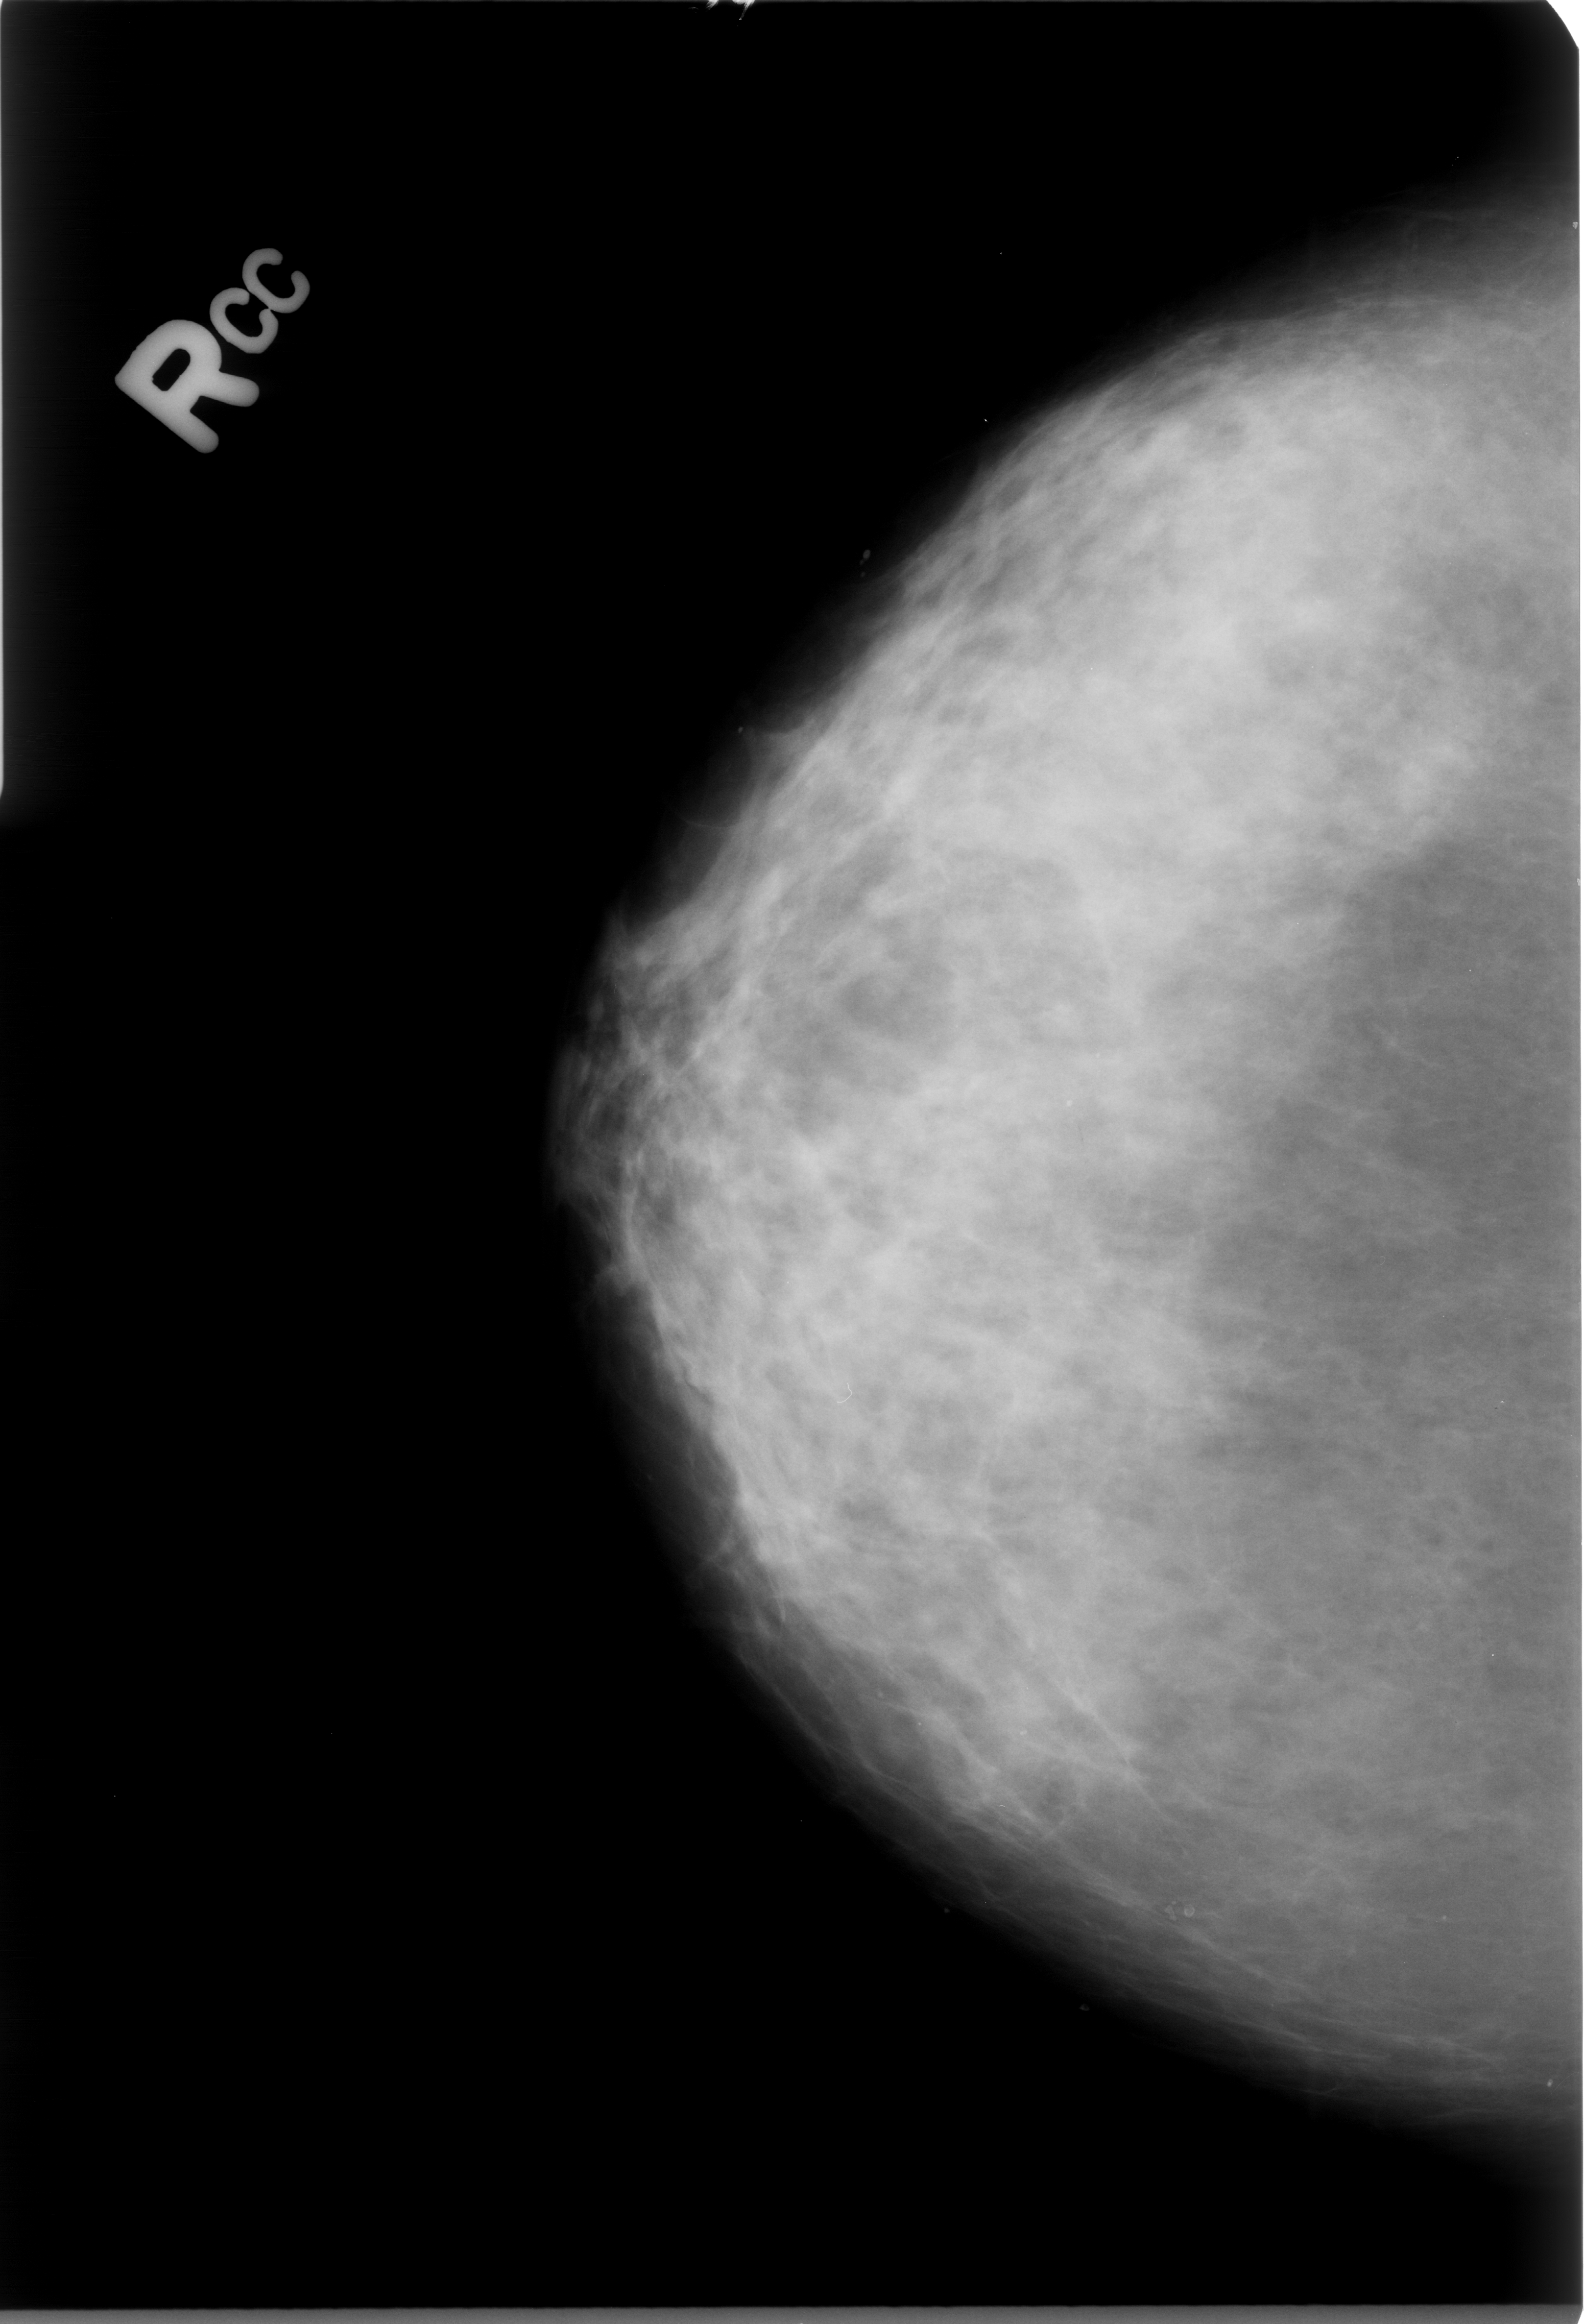
Digitized screen-film mammogram; right breast; CC view; breast composition: heterogeneously dense (BI-RADS density category 3 of 4); 1585 × 2324 image matrix.
Expert-marked regions of interest on this film, with their recorded descriptors:
- Finding 1 of 2: calcifications, morphology round and regular / lucent centered; BI-RADS assessment category 2; outcome (as recorded, no biopsy): benign without callback (not worked up further): box from (x=1053, y=1086) to (x=1088, y=1128) px
- Finding 2 of 2: calcifications, morphology round and regular / lucent centered; BI-RADS assessment category 2; subtlety rating 3 on a 1 (subtle) to 5 (obvious) scale; benign; no additional work-up was recommended (outcome (as recorded, no biopsy): benign without callback): (x=1180, y=1891)–(x=1206, y=1929)